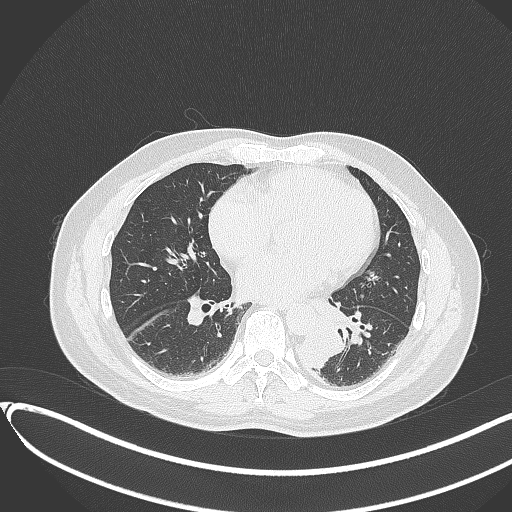
Chest CT, one axial slice; slice 140 of 417 in the series (ordered by position); reconstruction kernel B70f; 120 kVp; lung window (W 1500 / L -600 HU); 1 mm slice thickness; 512 × 512 image matrix. Male patient, age 54 years. Case-level facts recorded for this patient, not image findings: clinical TNM (as recorded): T3 N0 M0.
Annotated regions visible in this slice (bounding box drawn by a radiologist):
- lung tumour (recorded histology: squamous cell carcinoma): bounding box (x1, y1, x2, y2) in pixels: (291, 324, 346, 372)